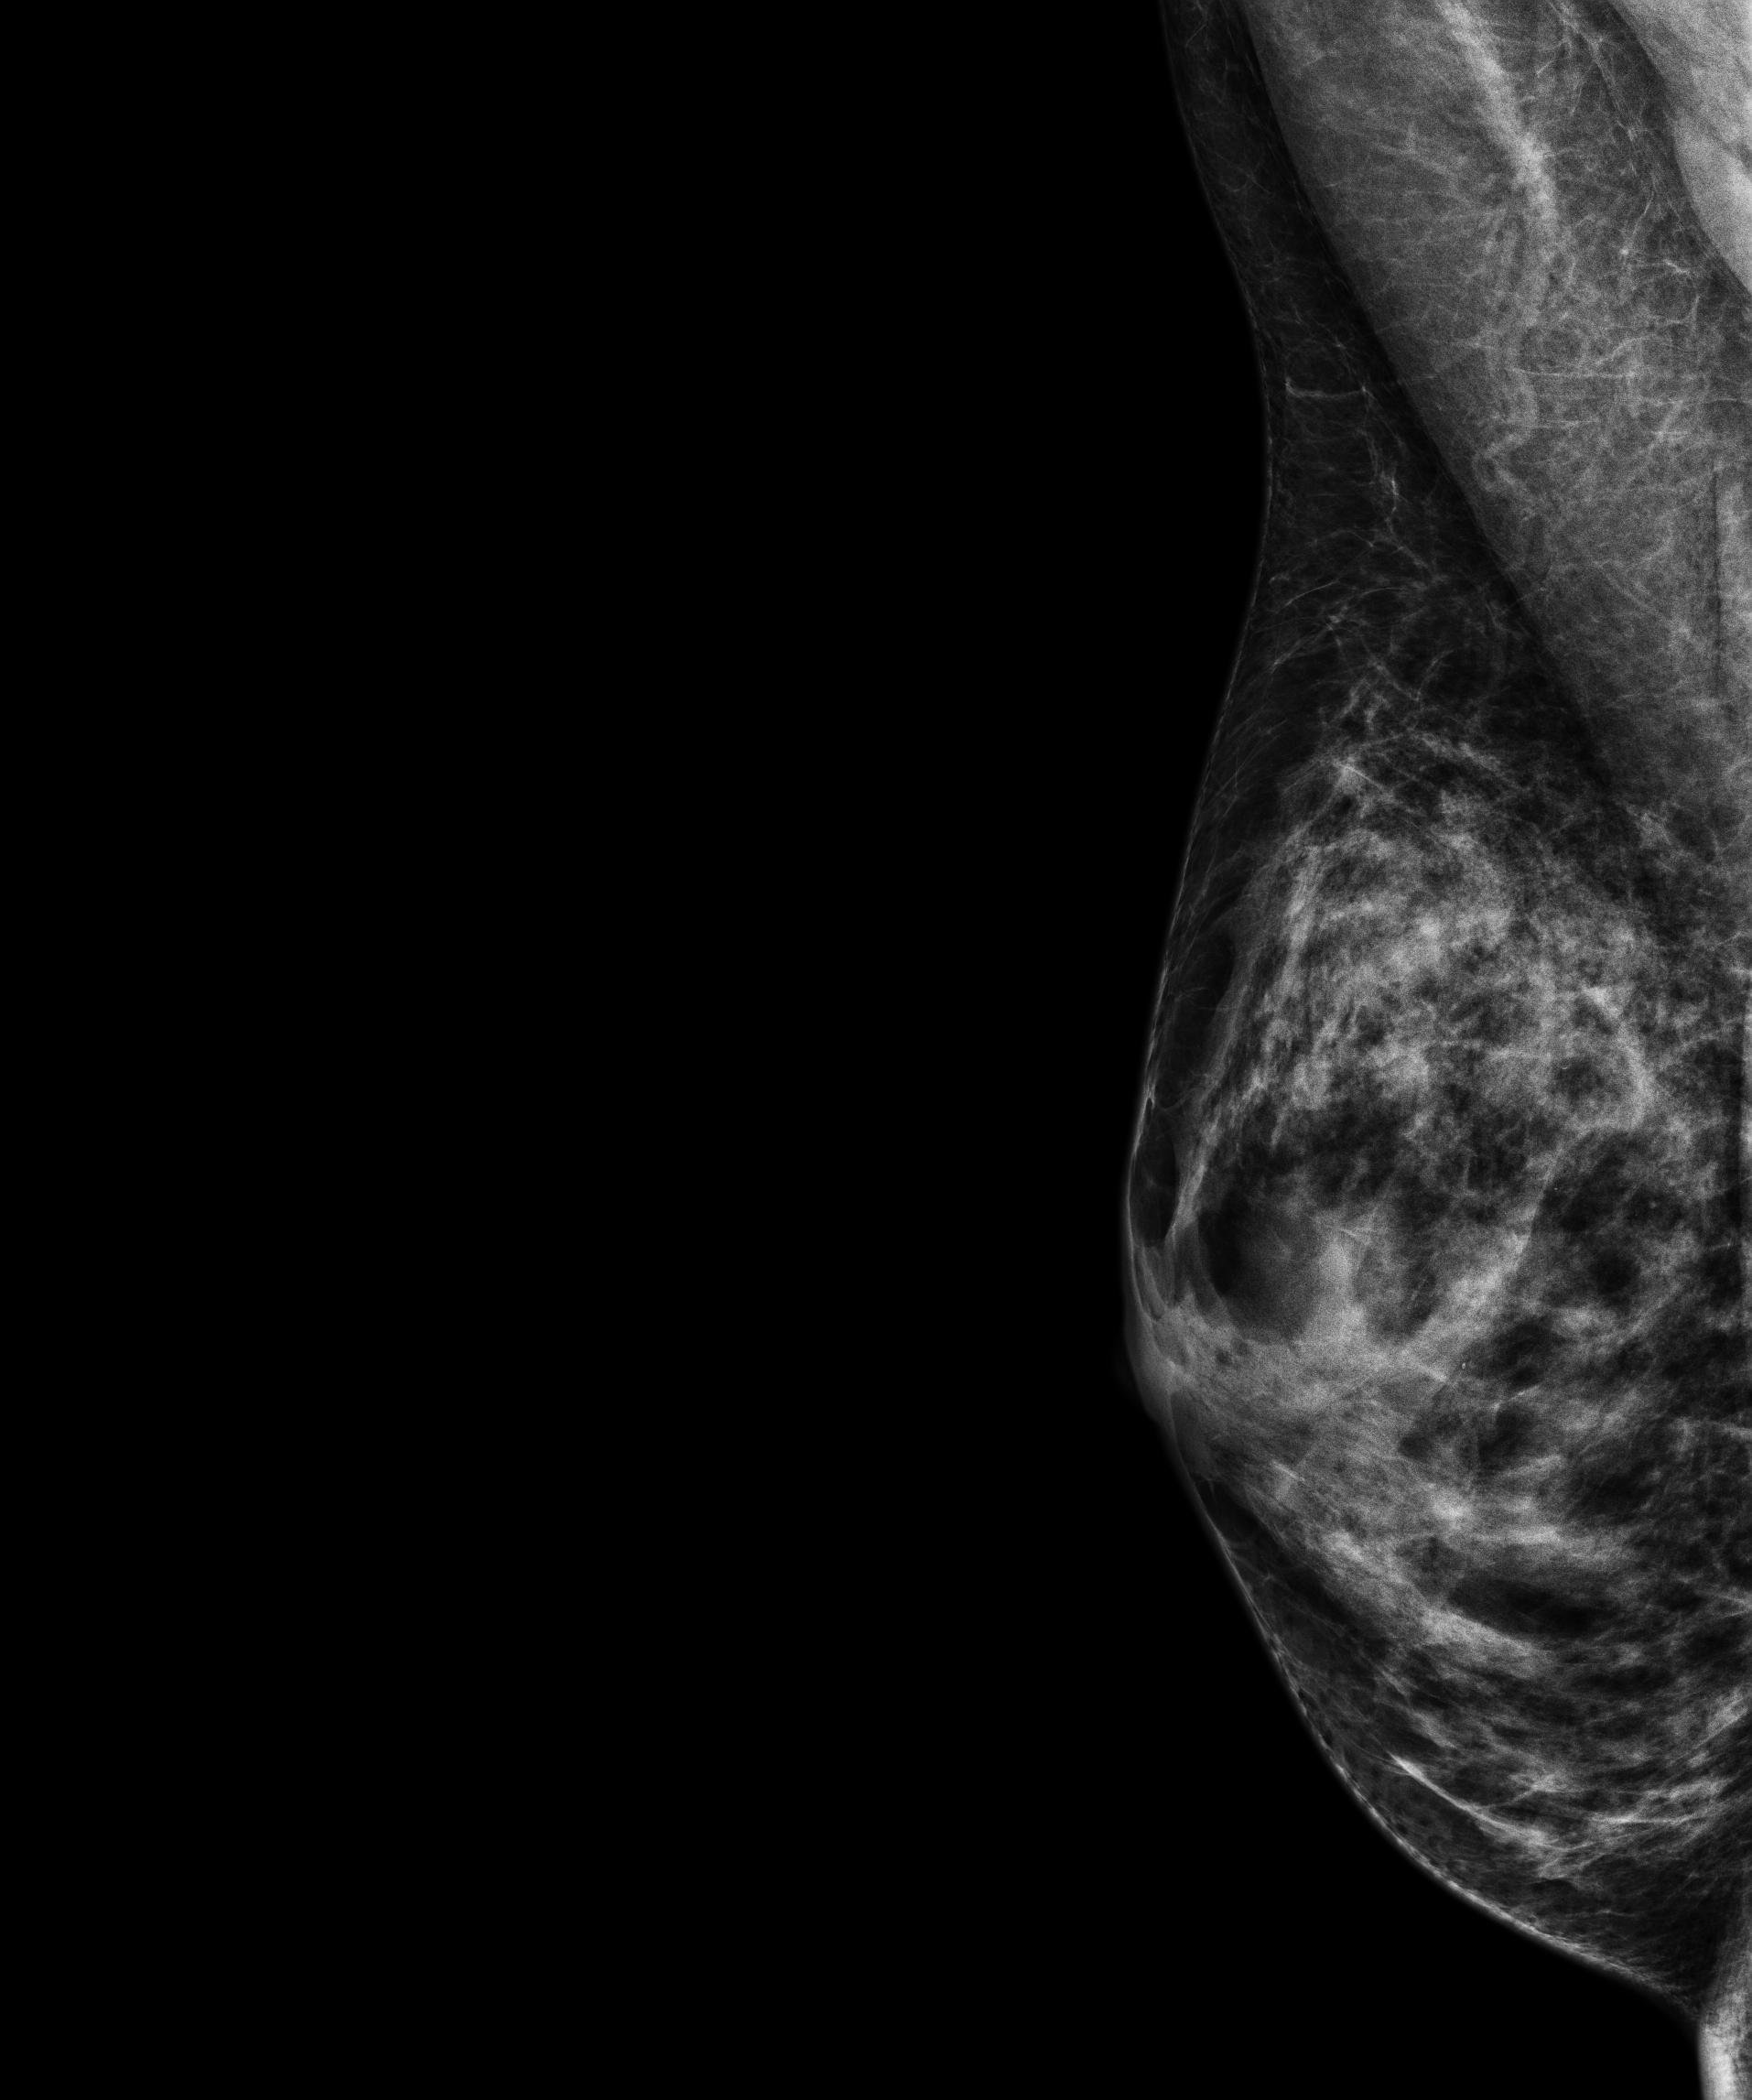
Screening examination, system: Senographe Pristina. Female patient, age 44 years.
Image type: full-field digital mammogram. Breast: right. Projection: MLO view.